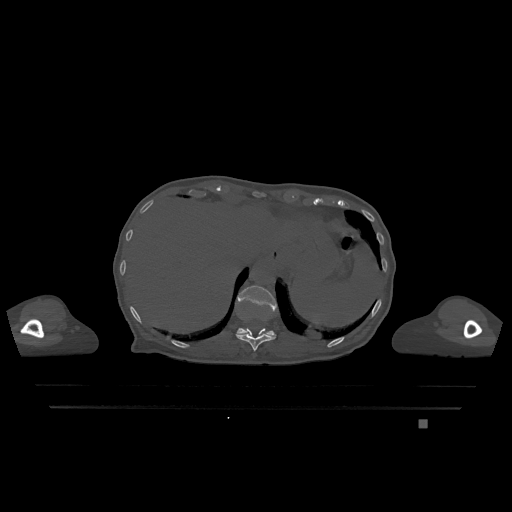
CT including the spine, one axial slice. Position 569 of 1317 along the scan axis. Bone window (W 1800 / L 400 HU). 0.5 mm slice thickness. 512 × 512 image matrix, field of view 500 × 500 mm. Patient: female, 74 years. From the clinical record (not read from this slice): primary cancer: lung.
Outlined on this slice (semi-automatically segmented with operator editing):
- T11 vertebra: bounding box (x1, y1, x2, y2) in pixels: (236, 328, 276, 351)
- T12 vertebra: (237, 285, 277, 337)